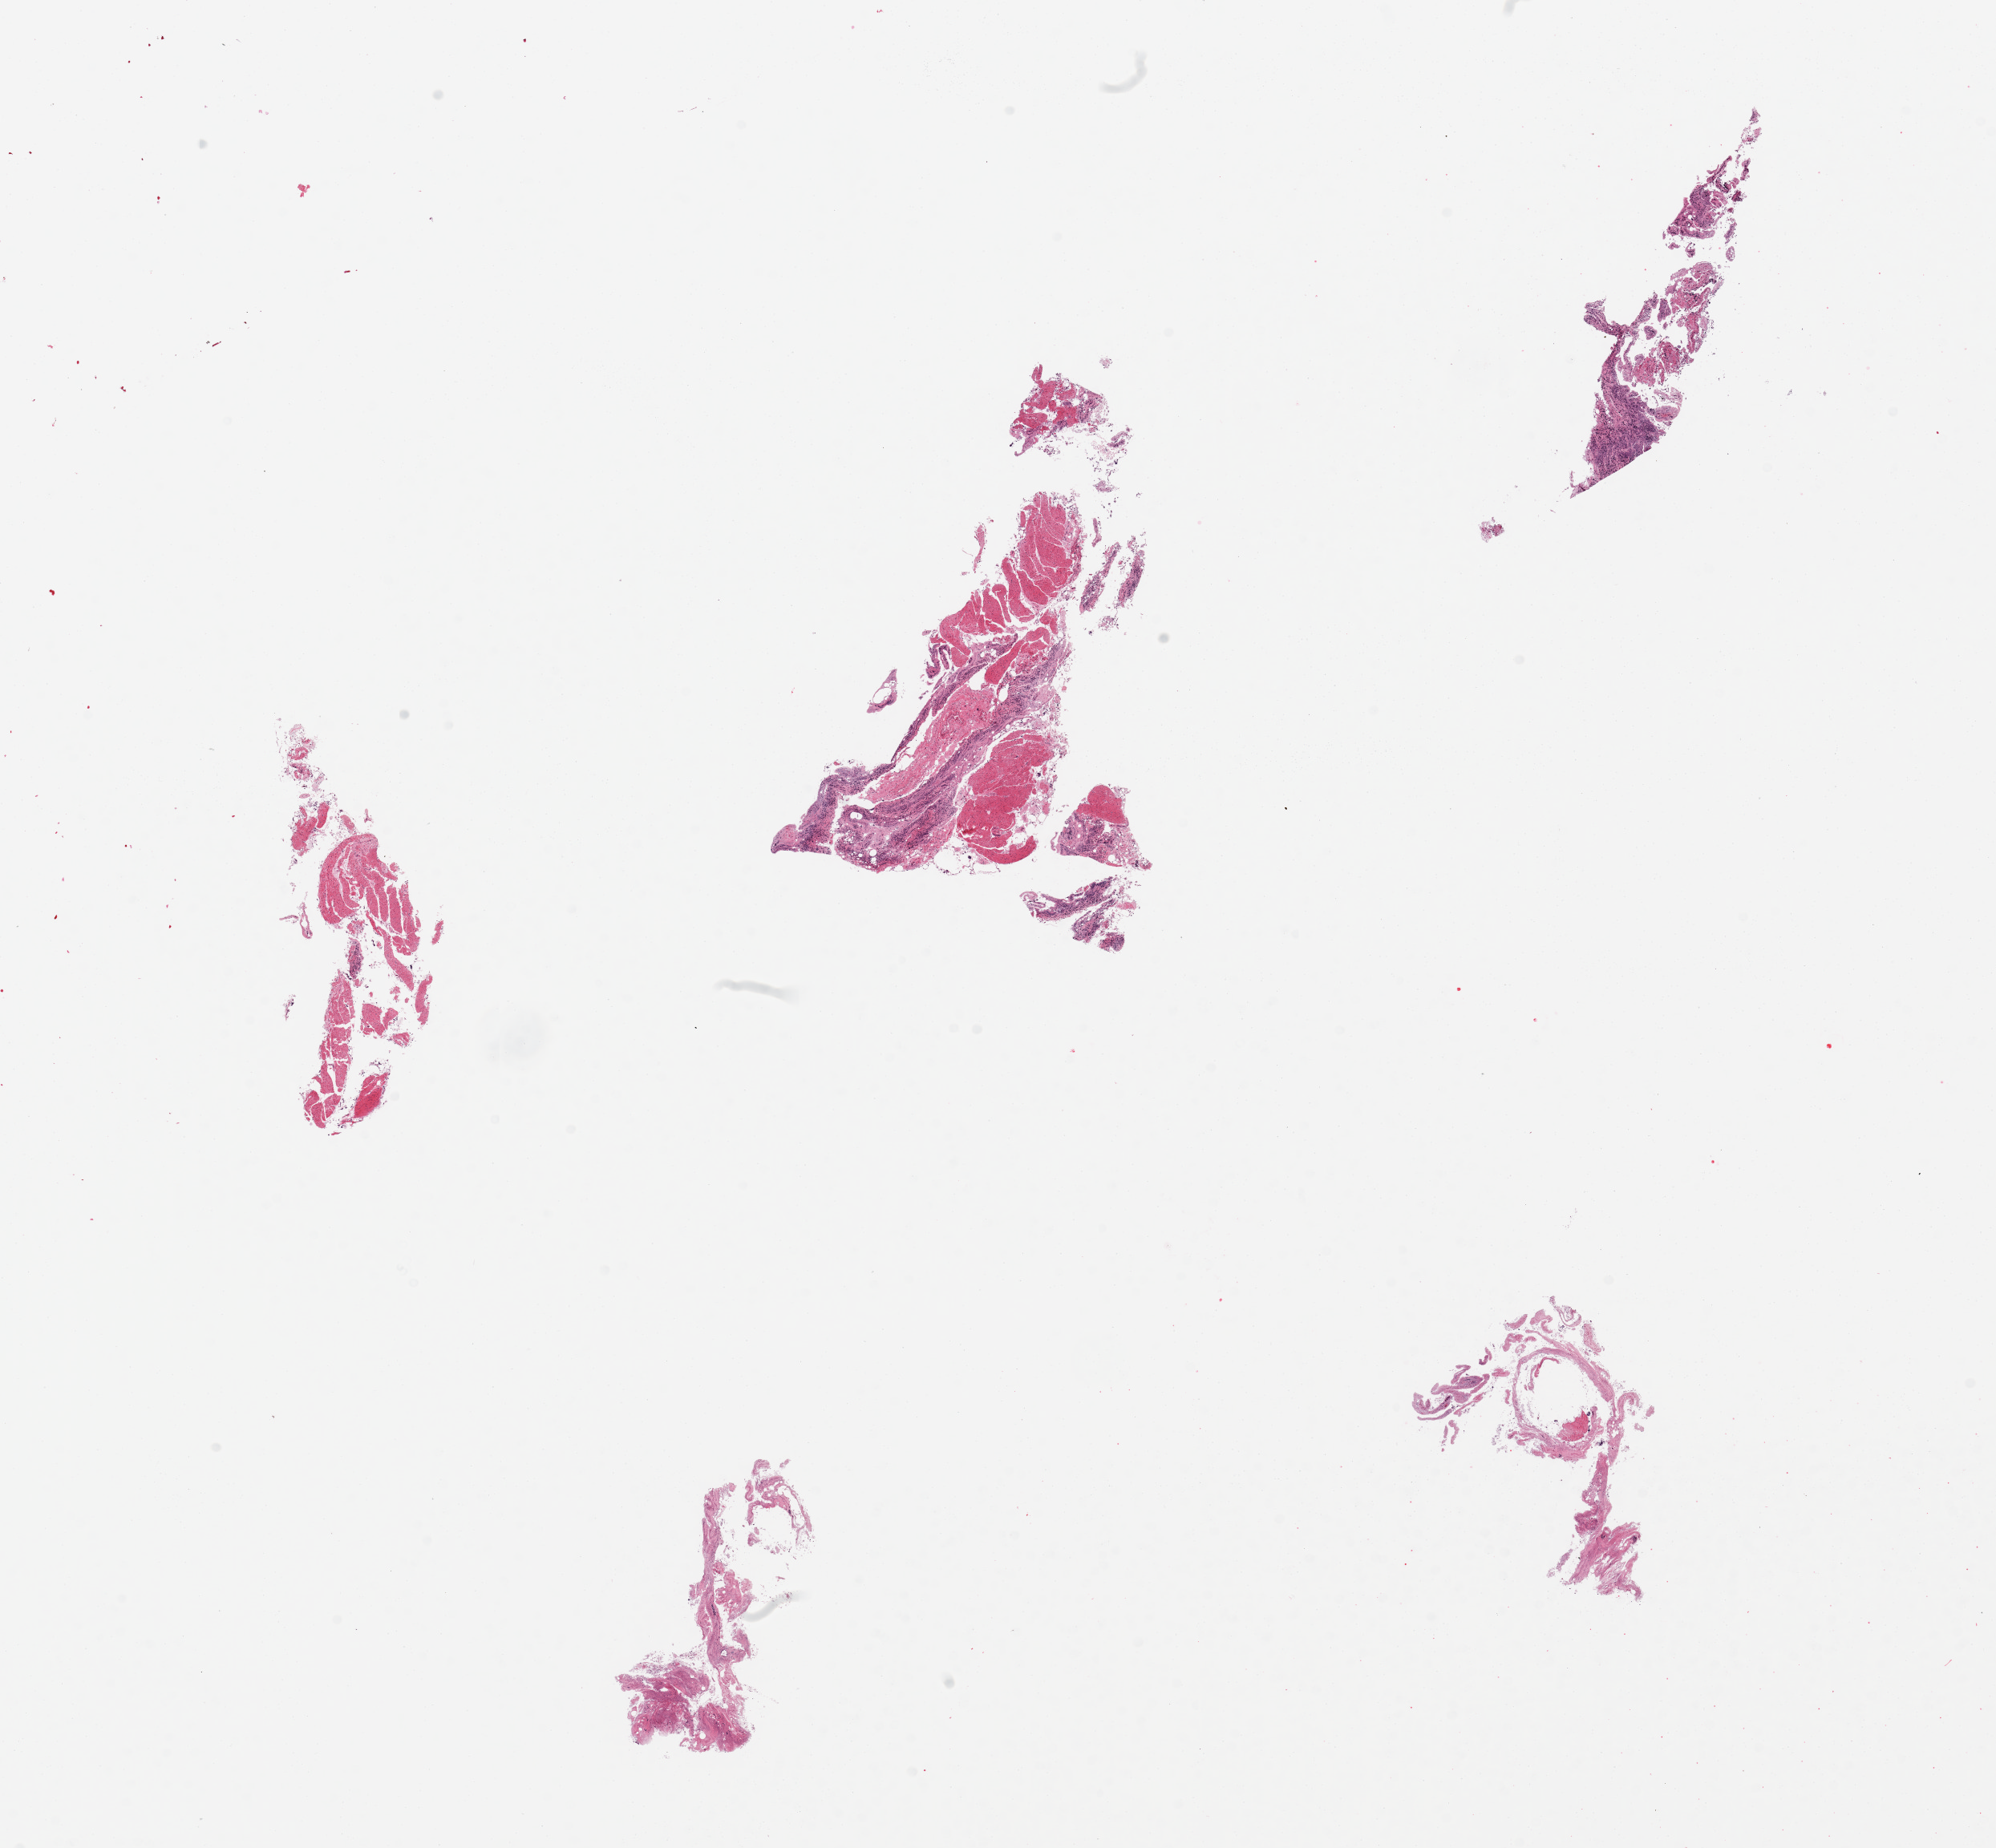
Whole-slide image, hematoxylin and eosin (H&E) stain, brightfield, whole scanned area (about 19.7 x 18.2 mm) shown as a low-resolution overview; PAXgene-fixed paraffin-embedded (PFPE) section; section of ileum (target tissue); tissue donor sample. Male donor.
Review note (as recorded): 5 pieces, trace fragments, autolyzed mucosa, no target lymphoid aggregates.